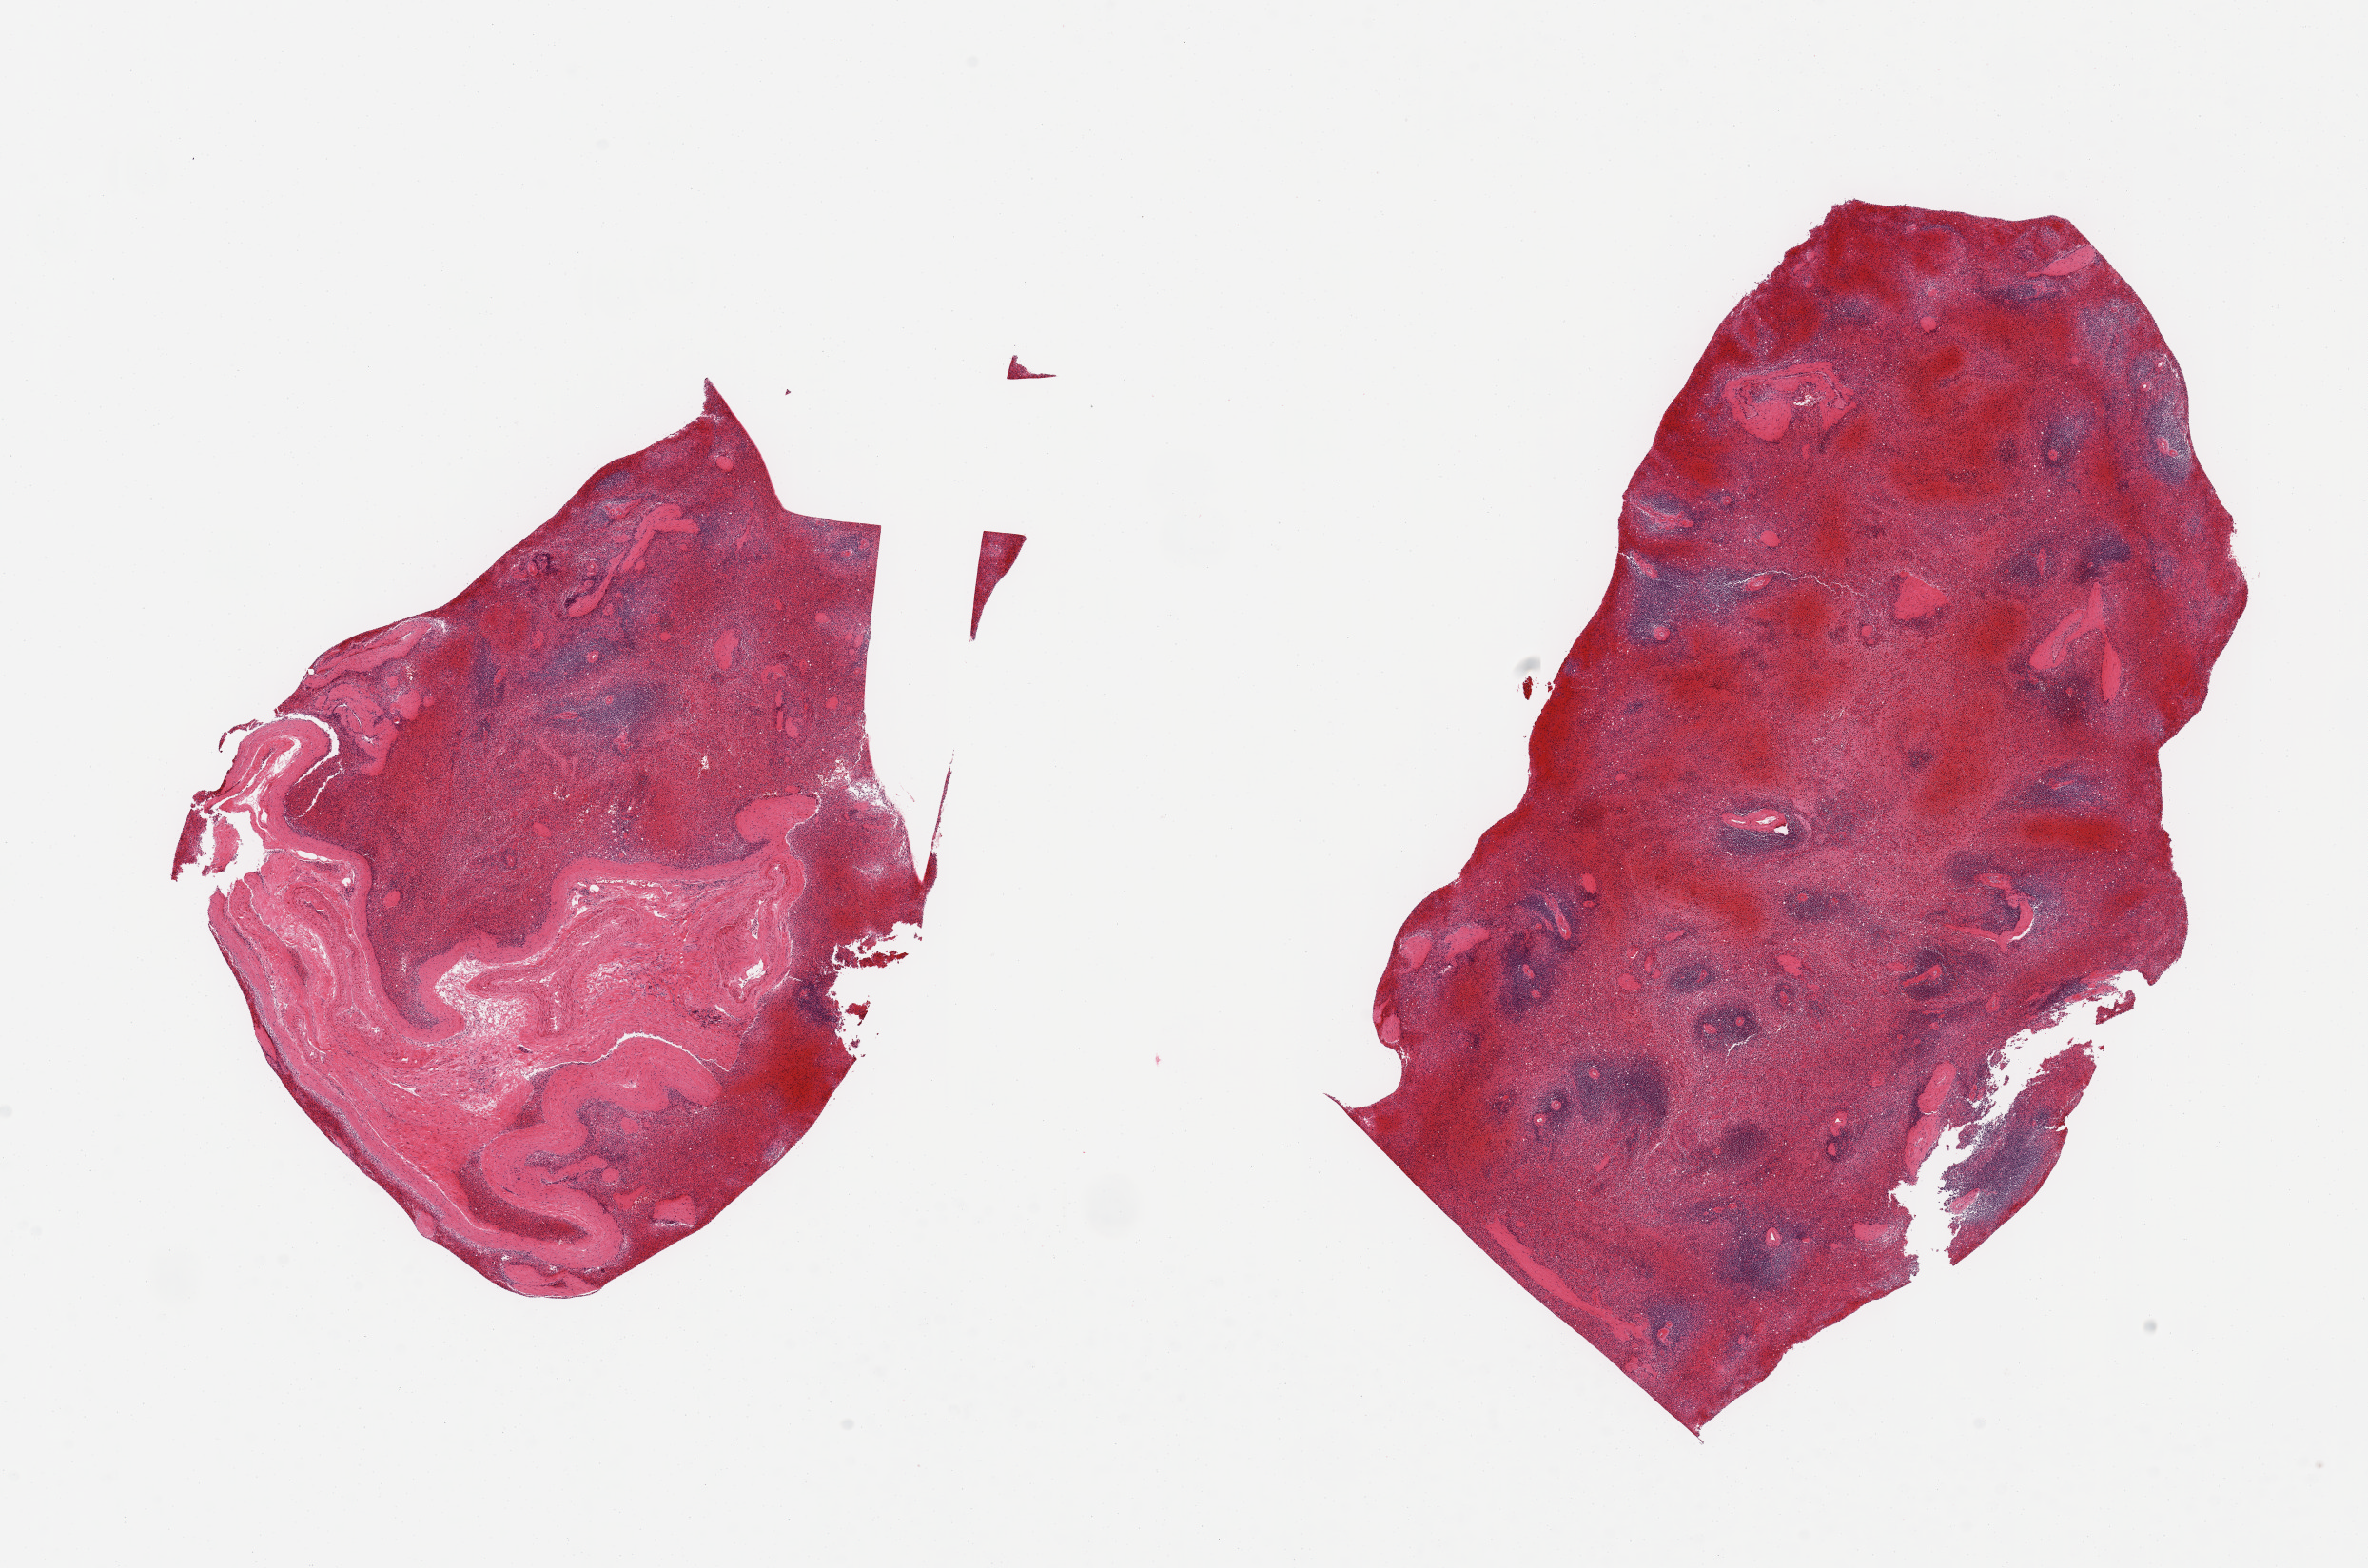
Whole-slide image, hematoxylin and eosin (H&E) stain, brightfield — a low-resolution overview of the entire scanned area, about 19.7 x 13.0 mm (from a 20x scan), PAXgene-fixed paraffin-embedded (PFPE) section, section of spleen (target tissue), donor tissue sample.
- pathologist's review note for this sample: 2 pieces; congestion; 1 piece is ~40% vessels/fibrous tissue